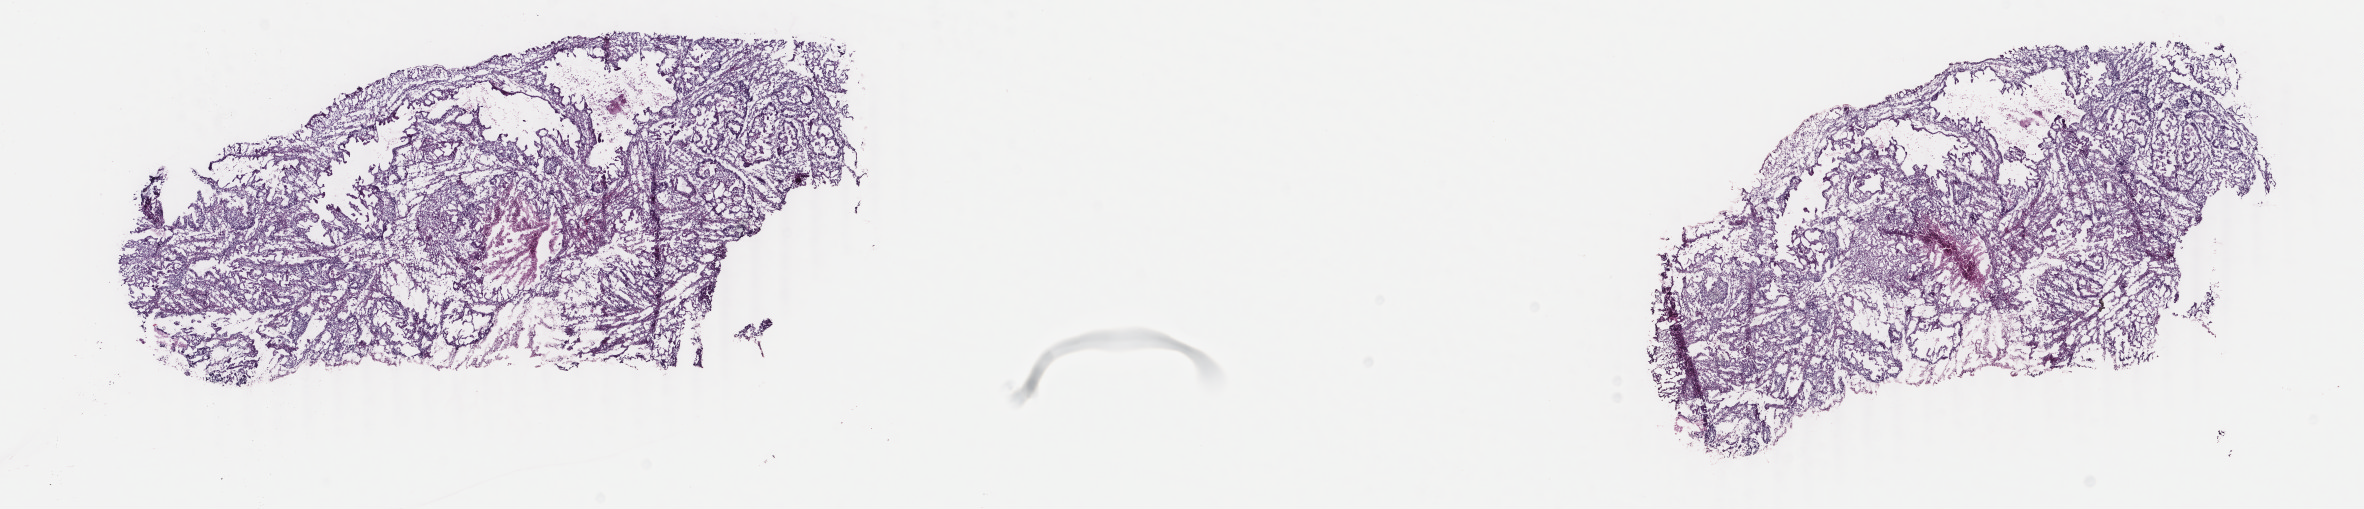
H&E-stained whole-slide image, low-resolution overview of the scanned area, about 18.8 x 4.0 mm, frozen section from the bottom of the tissue portion, uterus, primary tumour sample. Female patient; age at initial diagnosis 62 years. Histologic grade: G1 (well differentiated). Composition of this section per pathologist review: tumour cells 85%, tumour nuclei 95%, normal cells 0%, stromal cells 5%, necrosis 10%. Inflammatory infiltration, as recorded: lymphocyte infiltration 20%, monocyte infiltration 8%, neutrophil infiltration 8%.
* FIGO stage: IA
* pathologic diagnosis: Endometrioid adenocarcinoma, NOS